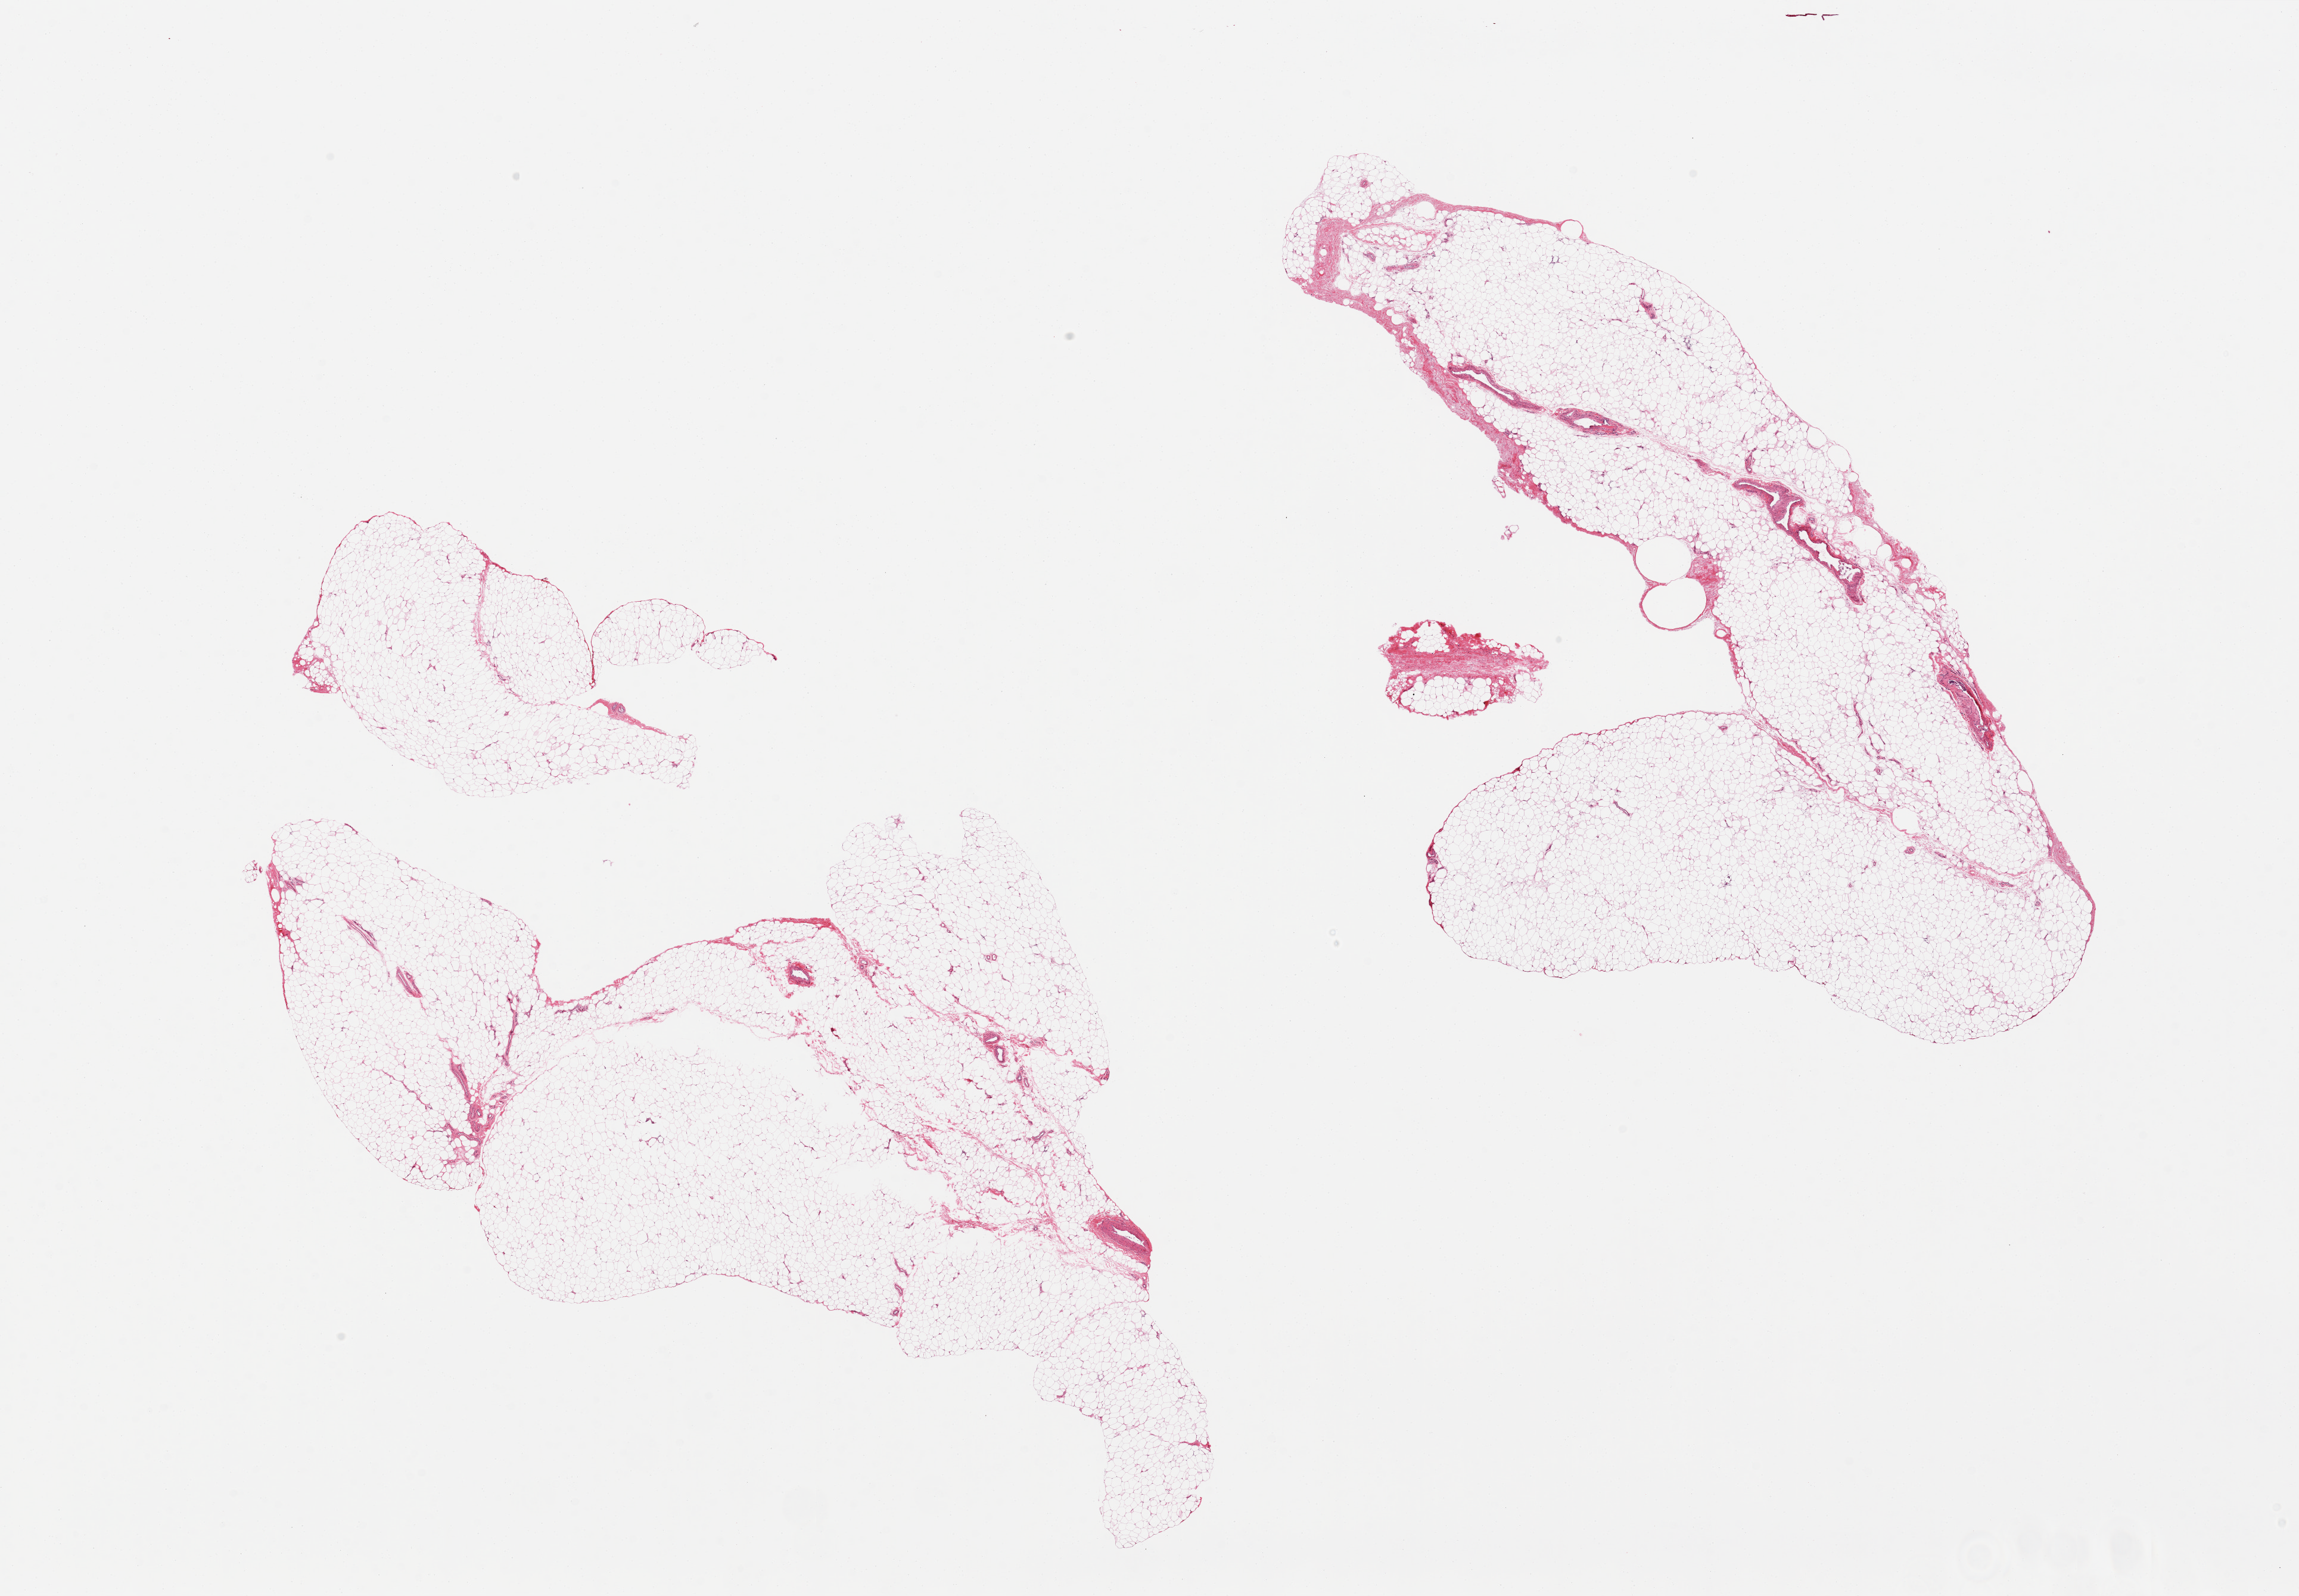
Hematoxylin and eosin (H&E) whole-slide image, brightfield — shown as a low-resolution overview of the whole scanned area (about 30.5 x 21.2 mm, from a 20x scan), PAXgene-fixed, paraffin-embedded tissue, section of adipose tissue (target tissue), tissue donor sample. Donor sex: male.
* review note (as recorded): 2 pieces (fragmented)